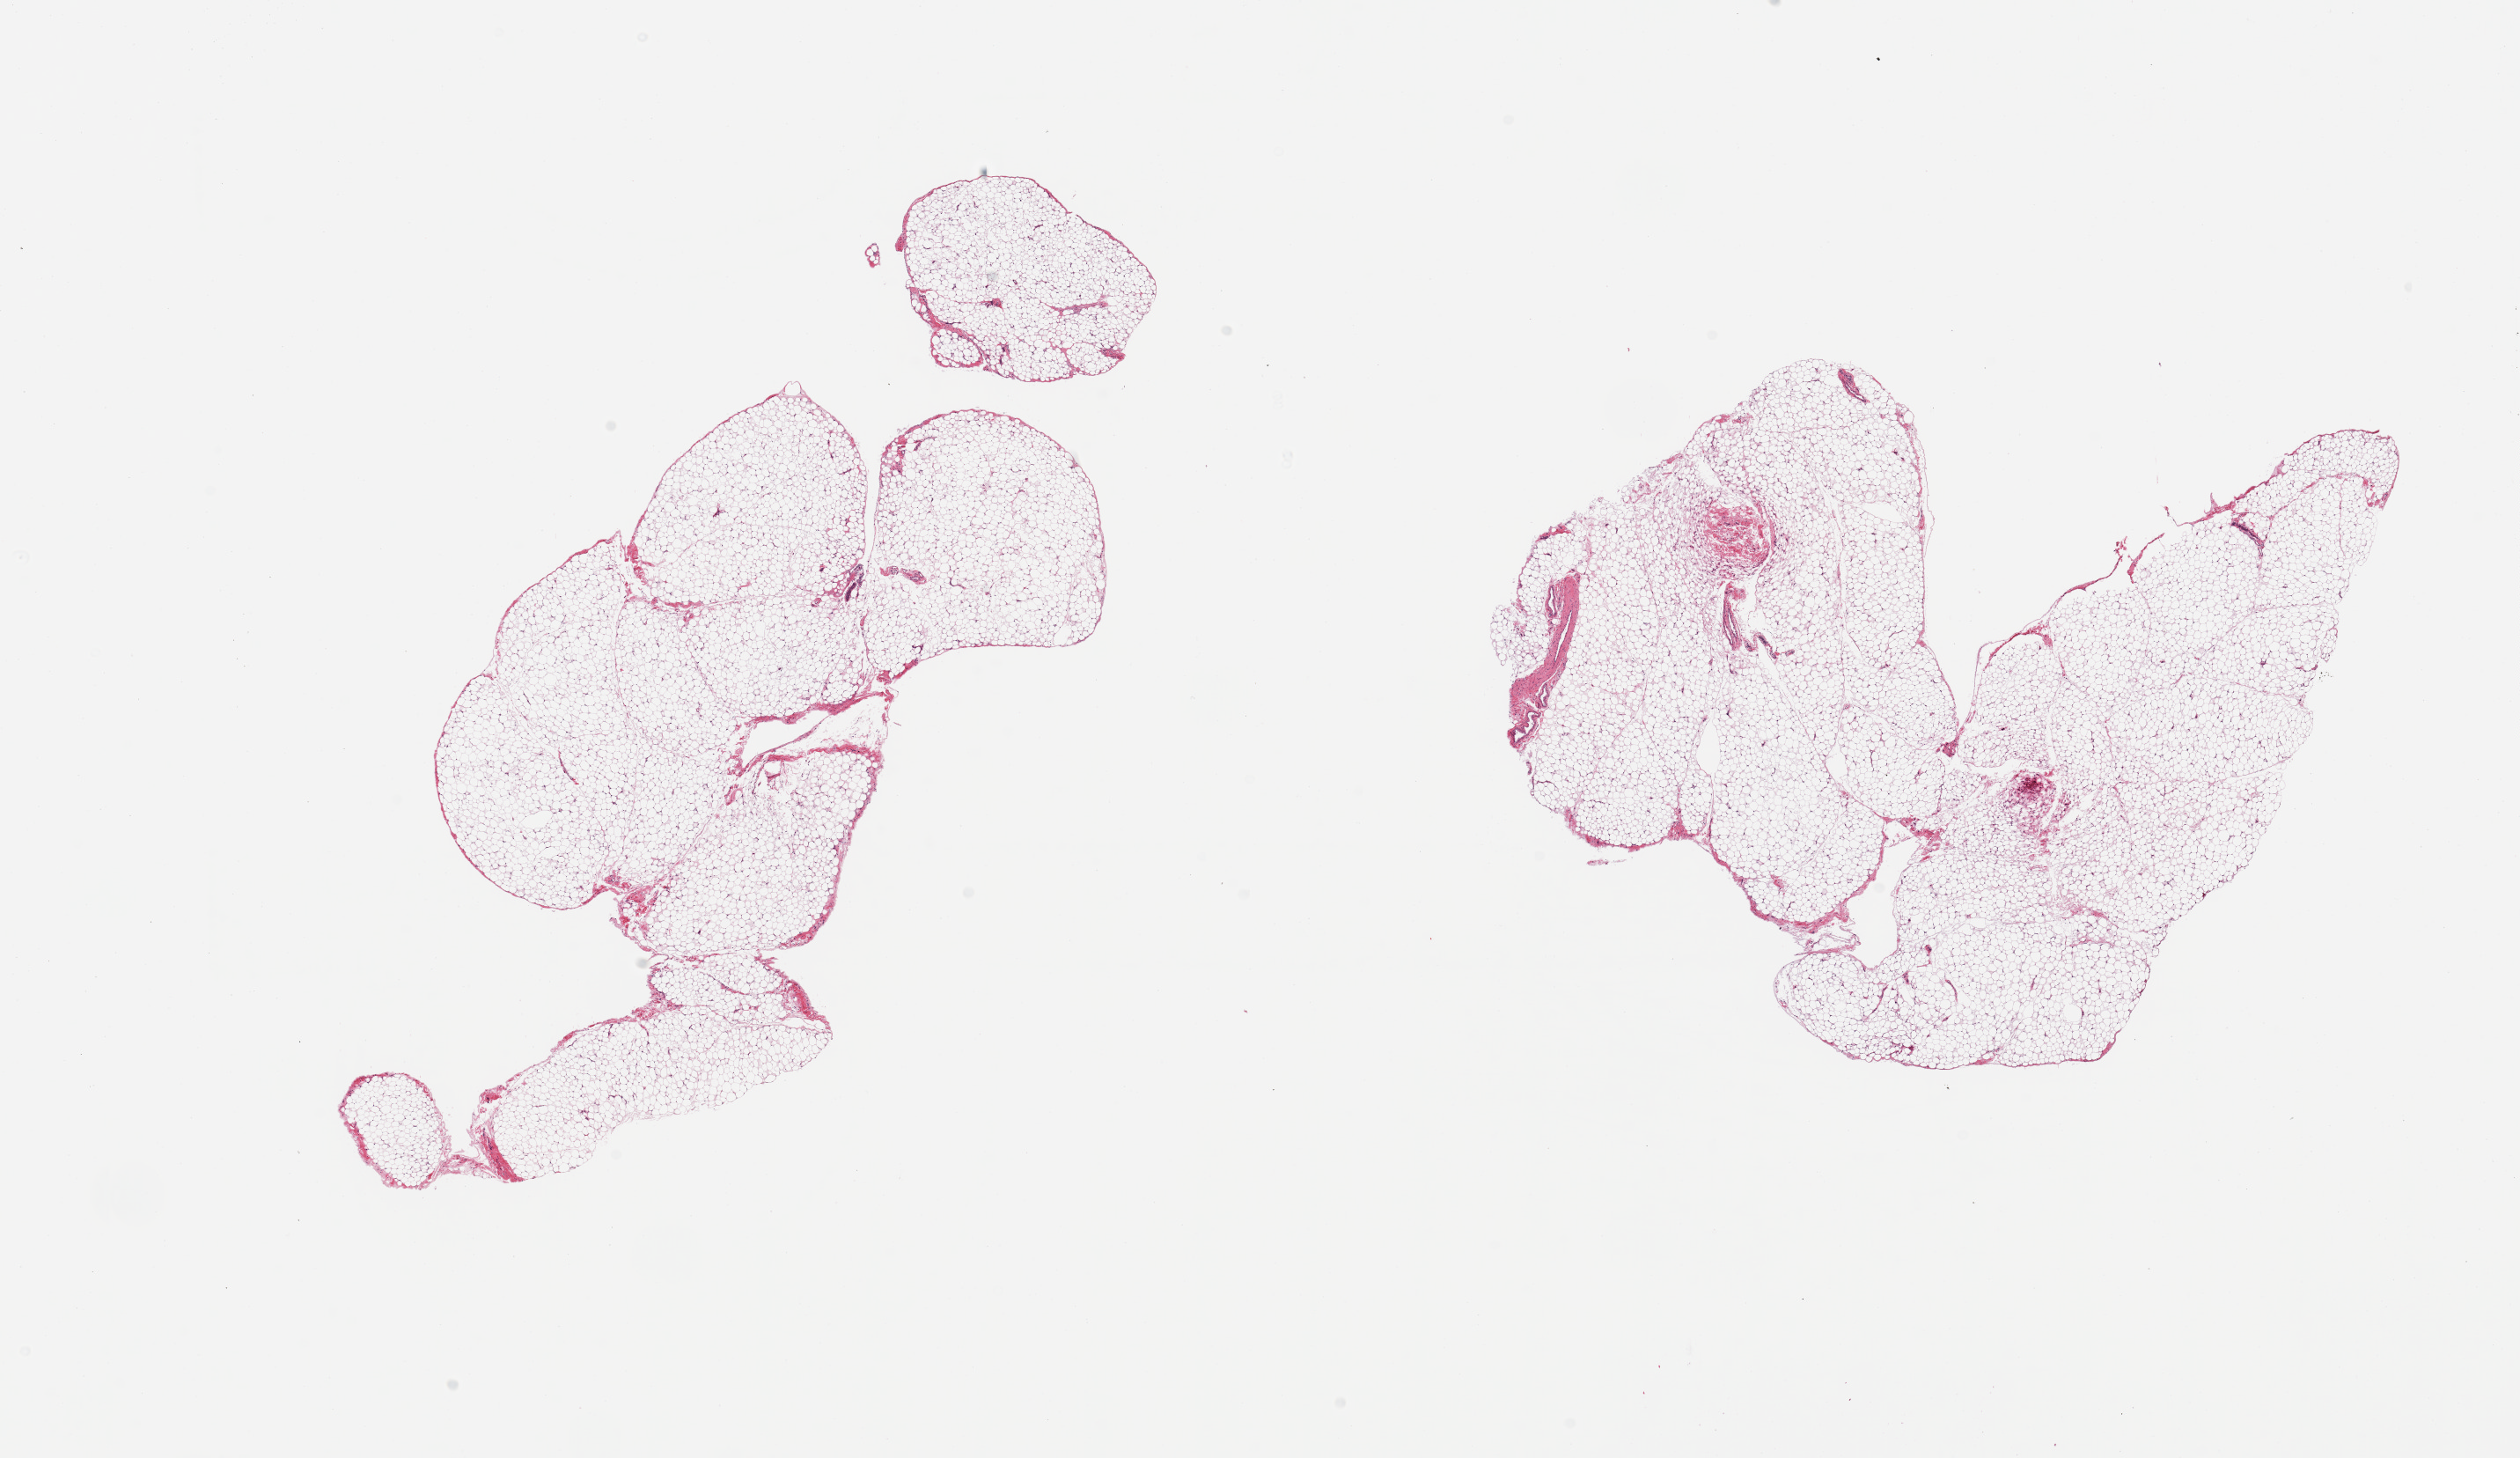
H&E whole-slide image — whole scanned area (about 22.6 x 13.1 mm, slide scanned at 20x) shown as a low-resolution overview. PAXgene-fixed paraffin-embedded (PFPE) section. Sampled site (target tissue): pancreas. Donor tissue sample. Donor: male.
Pathologist's review note for this sample: 2 pieces; adipose tissue NOT pancreas.